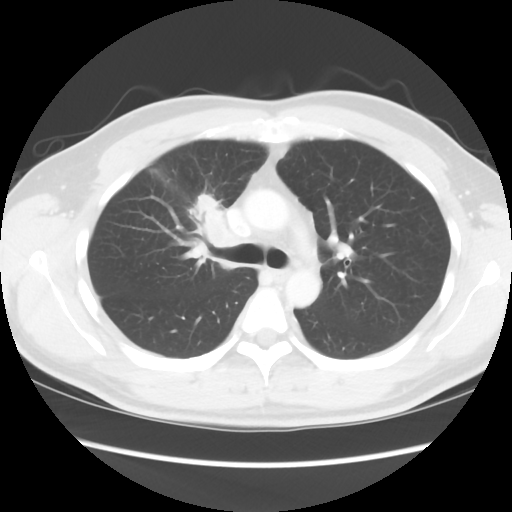
Chest CT, one axial slice. Slice 61 of 80 in the series (ordered by position). Reconstruction kernel STANDARD. Lung window (W 1500 / L -600 HU). 5 mm slice thickness. 512 × 512 image matrix, field of view 360 × 360 mm. Male patient, age 35 years. From the clinical record (not read from this slice): clinical TNM (as recorded): T1c N1 M1b.
Structures marked on this image (bounding box drawn by a radiologist):
- lung tumour (recorded histology: adenocarcinoma): bounding box [x1, y1, x2, y2] px = [190, 192, 229, 250]